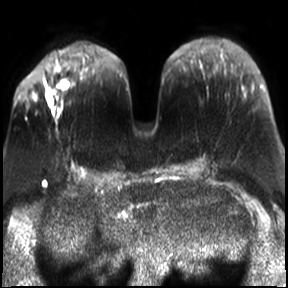
Breast MRI, one axial slice. Position 10 of 30 along the scan axis. Diffusion-weighted series; image 2 of 4 stored at this slice position (different b-values; order by instance number). 3 T. 288 × 288 image matrix, field of view 340 × 340 mm. Female patient.
Structures marked on this image (expert manual segmentation):
- tumour on diffusion-weighted imaging: bounding box <44,81,68,101> (left, top, right, bottom; pixels)